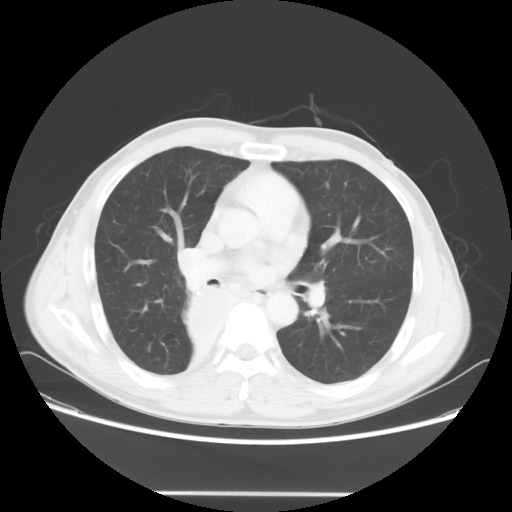
Chest CT, one axial slice. Slice 34 of 62 in the series (ordered by position). Reconstruction kernel STANDARD. 120 kVp. Lung window (W 1500 / L -600 HU). 5 mm slice thickness. 512 × 512 image matrix, field of view 393 × 393 mm. Patient: male, 47 years. From the clinical record (not read from this slice): clinical TNM (as recorded): T2 N0 M0.
Outlined on this slice (rectangle marked by the reading radiologist):
- lung tumour (recorded histology: squamous cell carcinoma): bounding box [x1, y1, x2, y2] px = [175, 283, 233, 359]